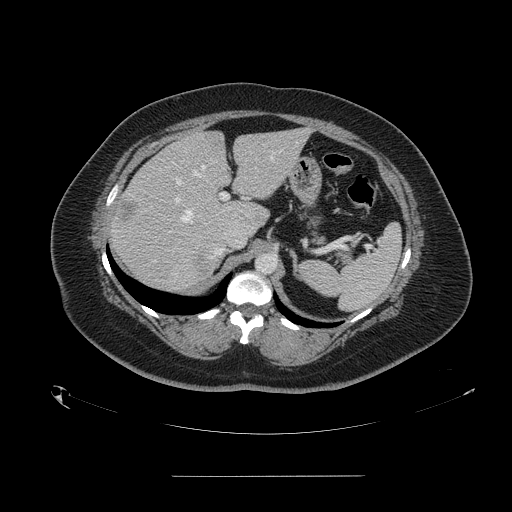
Contrast-enhanced abdominal CT, one axial slice; slice 102 of 164 in the series (ordered by position); 120 kVp; intravenous contrast given; soft-tissue window (W 400 / L 40 HU); 2.5 mm slice thickness; 512 × 512 image matrix, field of view 495 × 495 mm. Female patient, age 52 years. Case-level facts recorded for this patient, not image findings: diagnosis: colorectal cancer liver metastases, imaged before liver resection; multiple liver metastases: yes.
Annotated regions visible in this slice (expert manual segmentation):
- hepatic veins: bounding box [x1, y1, x2, y2] px = [181, 157, 273, 222]
- liver: [111, 130, 308, 291]
- planned liver remnant (the part of the liver to remain after resection): [174, 129, 308, 229]
- portal vein (with intrahepatic branches): [174, 177, 229, 203]
- liver metastasis: [195, 253, 209, 276]
- liver metastasis: [251, 213, 264, 224]
- liver metastasis: [119, 202, 138, 225]